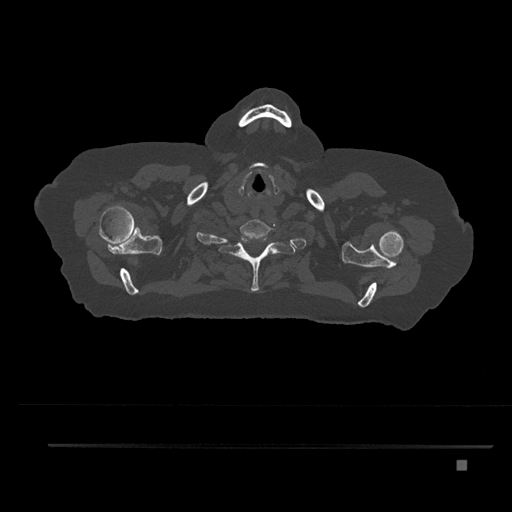
CT including the spine, one axial slice. Slice 705 of 797 in the series (ordered by position). Reconstruction kernel Br40s/3. Bone window (W 1800 / L 400 HU). 512 × 512 image matrix. Female patient, age 76 years. Case-level facts recorded for this patient, not image findings: primary cancer: lung.
Annotated regions visible in this slice (semi-automatically segmented with operator editing):
- T1 vertebra: bounding box [x1, y1, x2, y2] px = [224, 233, 283, 292]